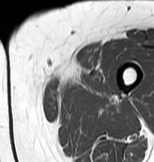
MRI of an extremity soft-tissue mass, one axial slice; position 6 of 83 along the scan axis; MR volume resampled by the dataset authors to the PET/CT grid (not the native acquisition matrix); 154 × 162 image matrix, field of view 150 × 158 mm. Female patient. Case-level facts recorded for this patient, not image findings: histological type: myxofibrosarcoma; grade: intermediate; site of the primary tumour: left thigh.
Structures marked on this image (expert contour drawn on MRI and transferred to this co-registered scan by the dataset authors):
- gross tumour volume including surrounding oedema: box from (x=46, y=61) to (x=109, y=99) px